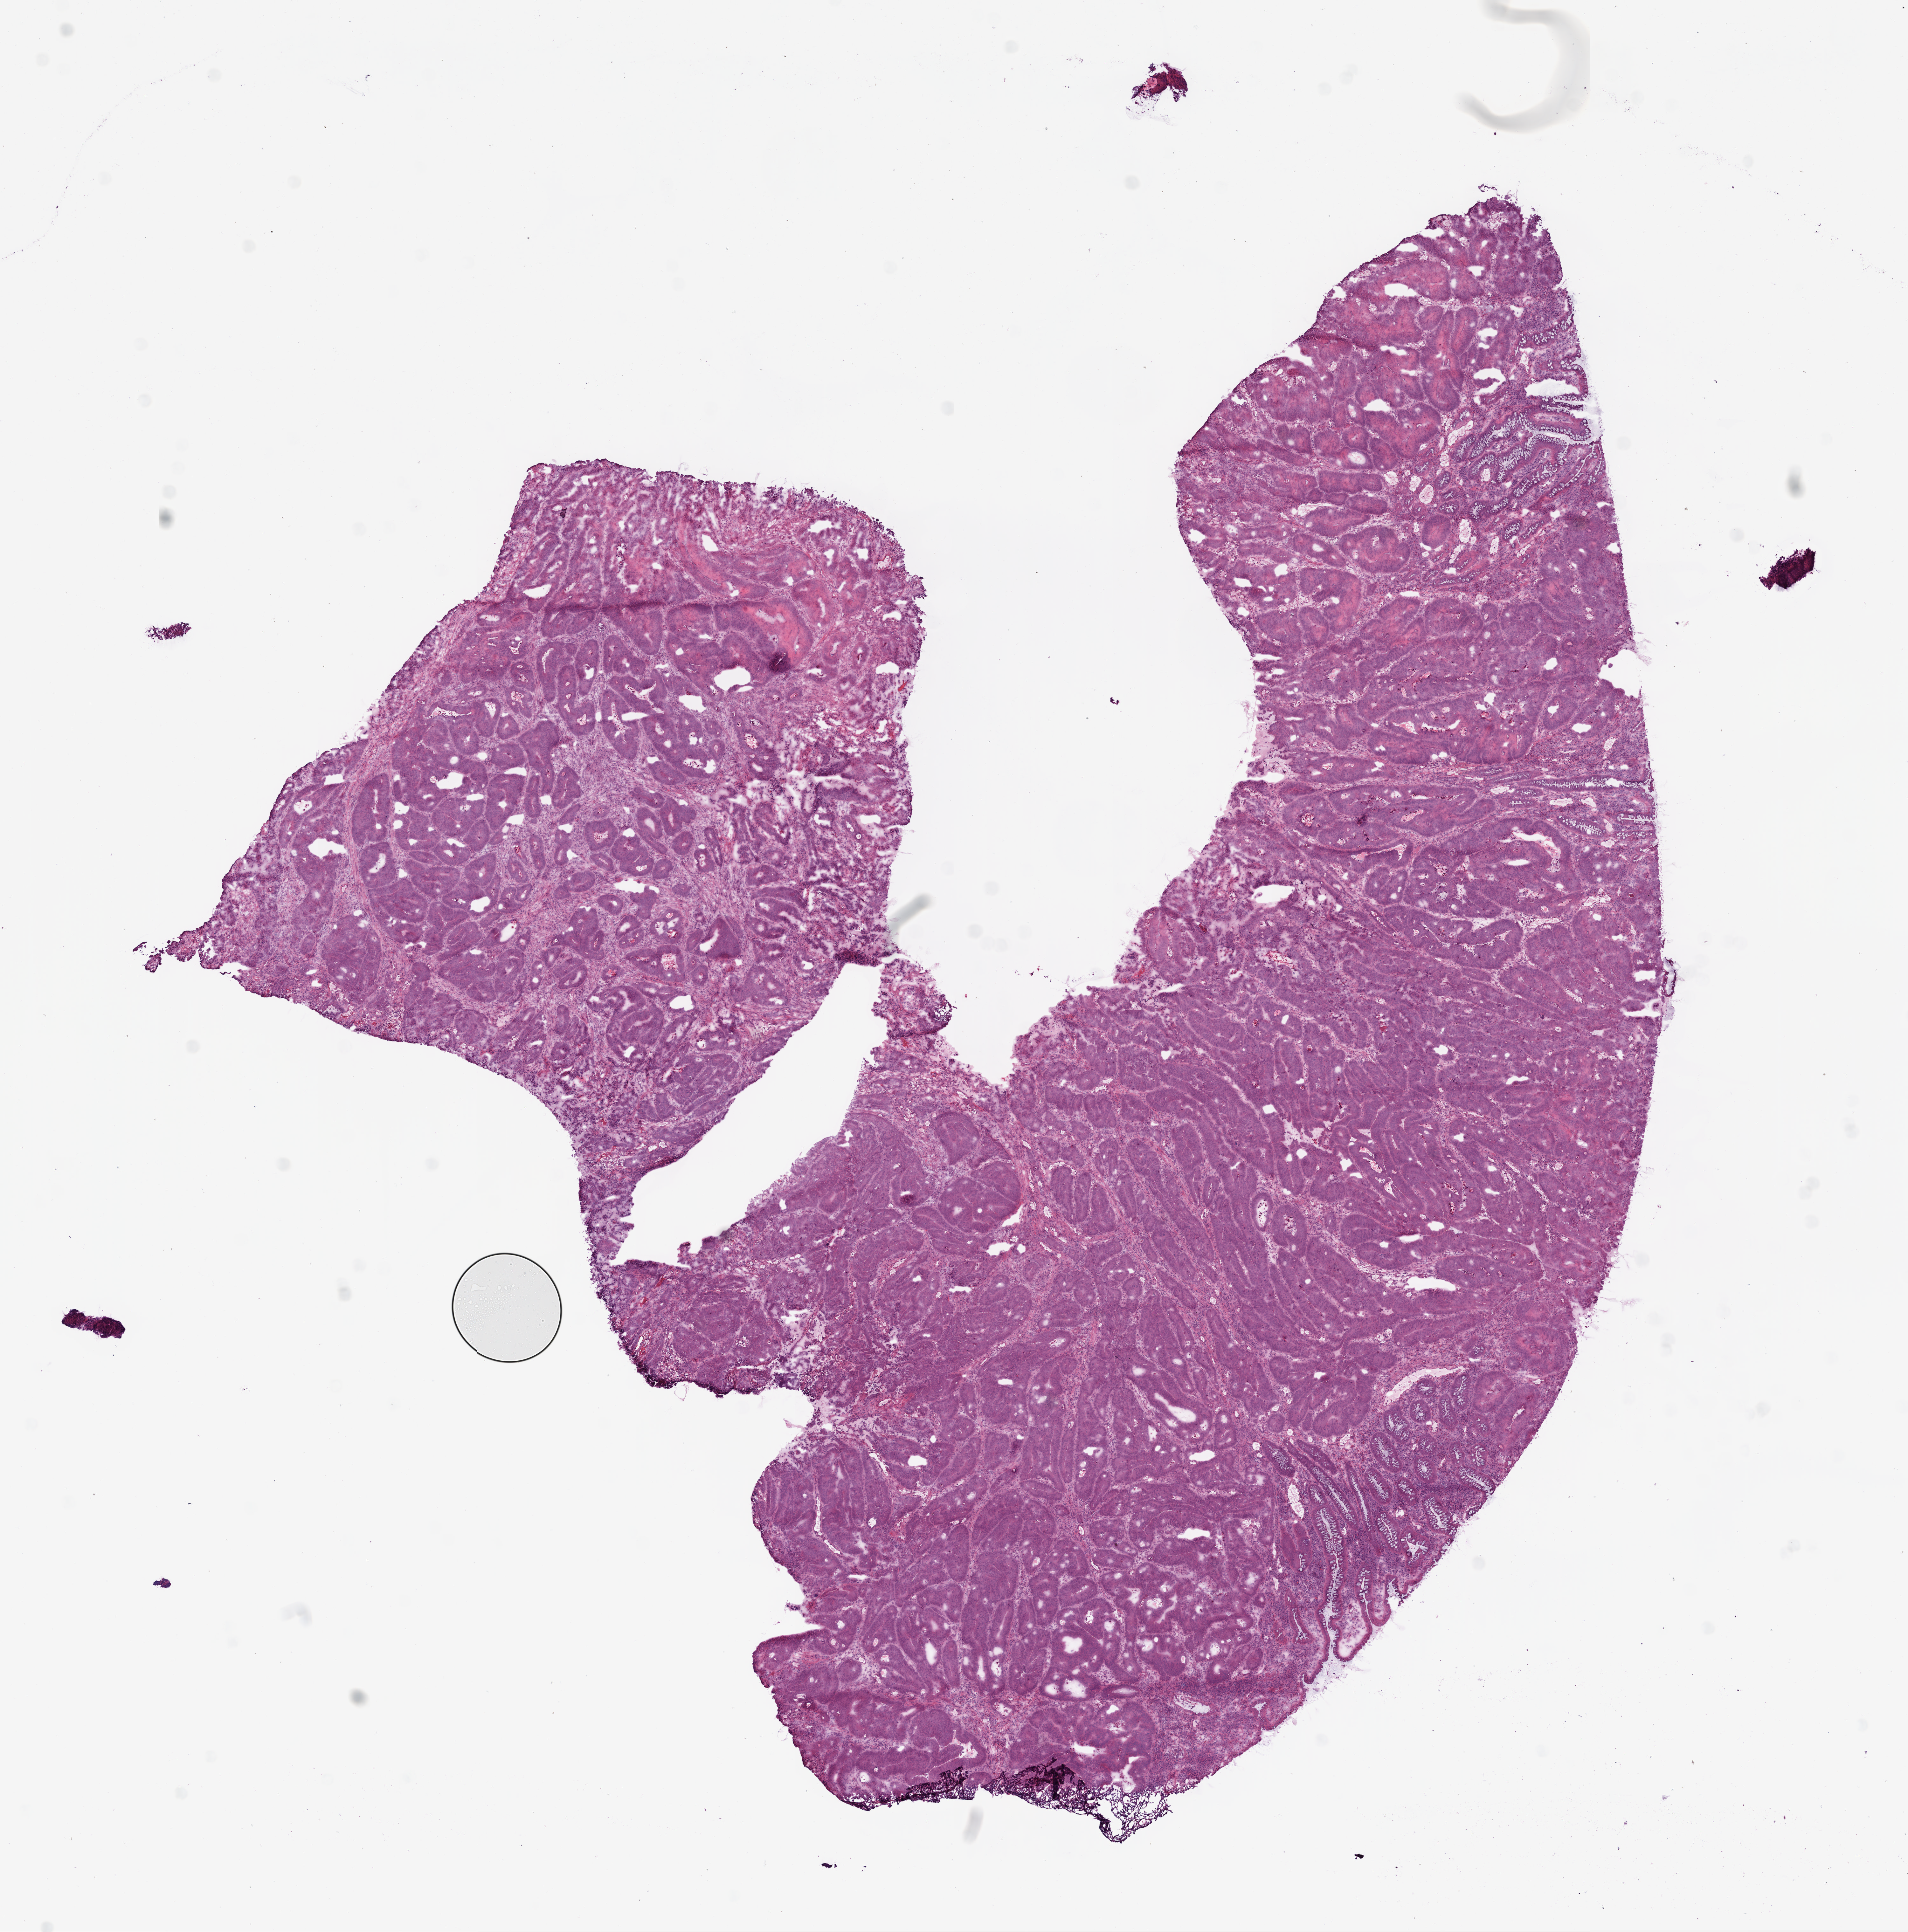
Whole-slide histology image, H&E, a low-resolution overview of the entire scanned area, about 12.0 x 12.2 mm, frozen section, sample: primary tumour, colon. Patient: male, age at initial diagnosis 69 years. Pathologist review of this section (percent, as recorded): tumour cells 84%, tumour nuclei 75%, normal cells 1%, stromal cells 10%, necrosis 5%.
AJCC pathologic stage: II (5th edition). Histologic diagnosis: Adenocarcinoma, NOS.